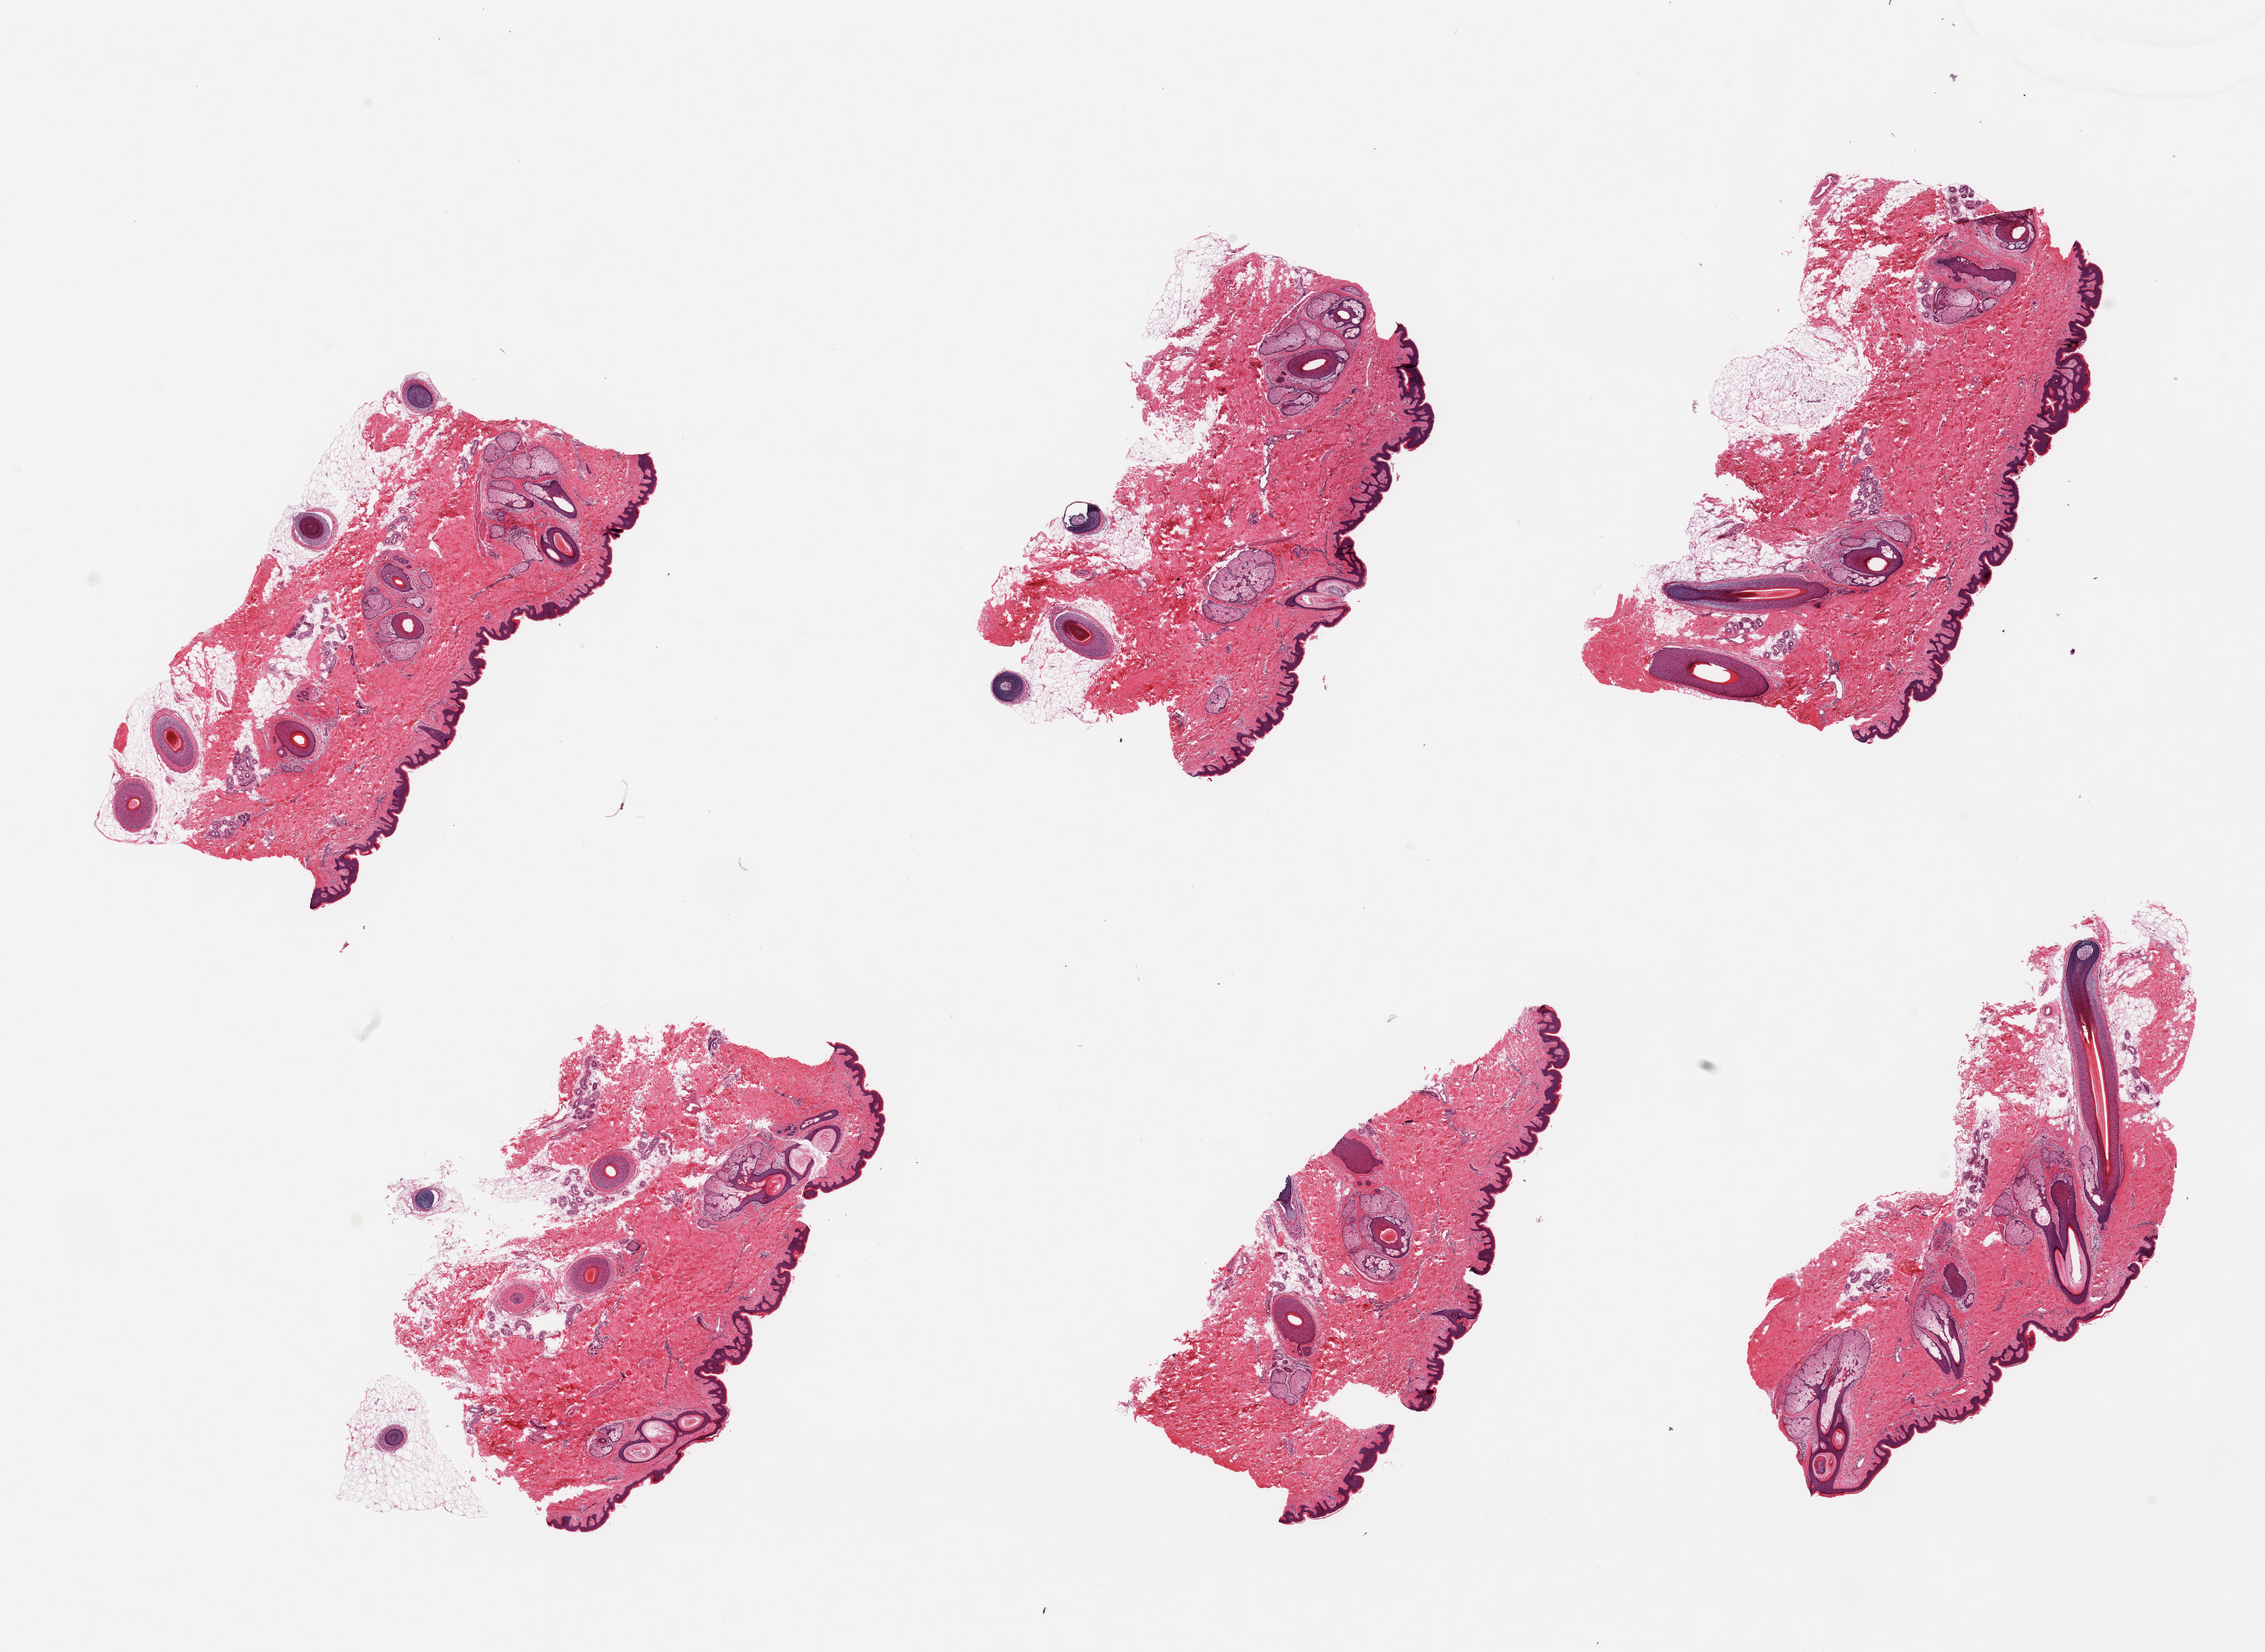
Hematoxylin and eosin (H&E) whole-slide image, shown as a low-resolution overview of the whole scanned area (about 24.6 x 18.0 mm, from a 20x scan); PAXgene-fixed paraffin-embedded (PFPE) section; section of skin of suprapubic region (target tissue); donor tissue sample. Donor sex: male.
Review note (as recorded): 6 pieces; well dissected; numerous hair follicles (up to 9 per piece).